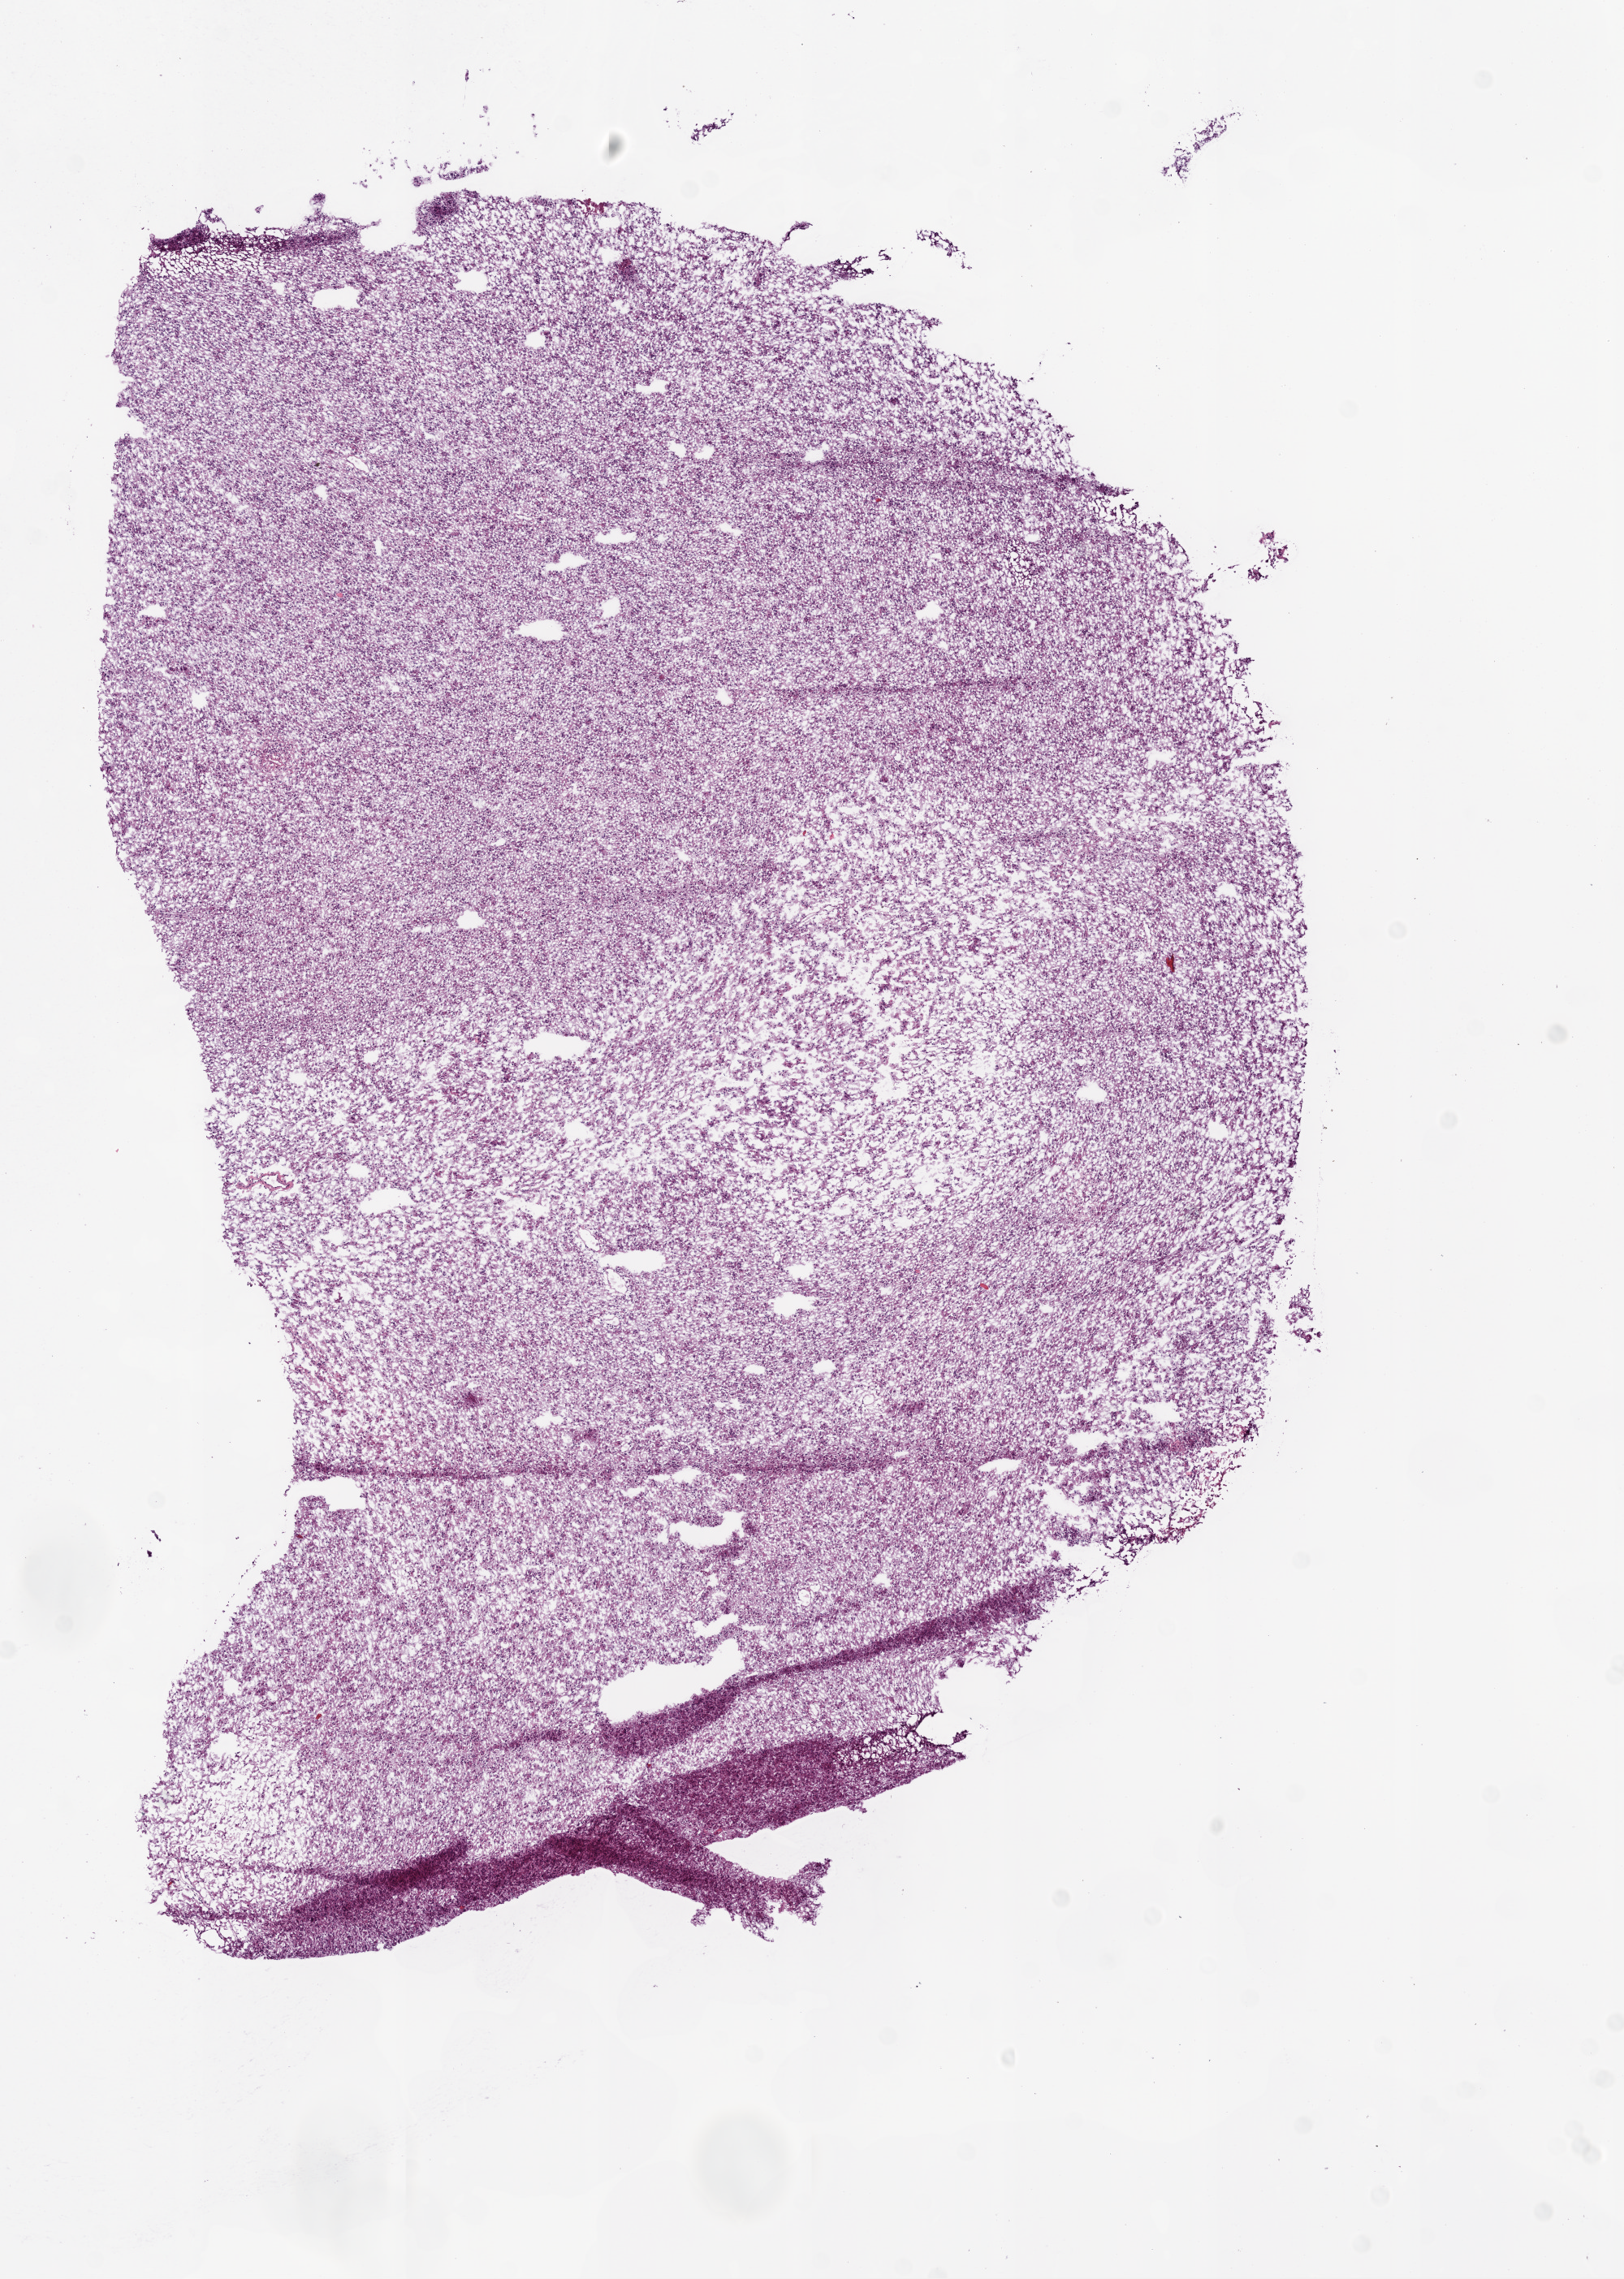
H&E whole-slide image, a low-resolution overview of the entire scanned area, about 8.0 x 11.3 mm (acquisition: 20x scan); frozen section from the bottom of the tissue portion; sample: primary tumour, brain. Female patient; age at initial diagnosis 82 years. Slide review estimates, as recorded: tumour cells 90%, tumour nuclei 95%, normal cells 0%, stromal cells 10%, necrosis 0%.
* diagnosis: Glioblastoma